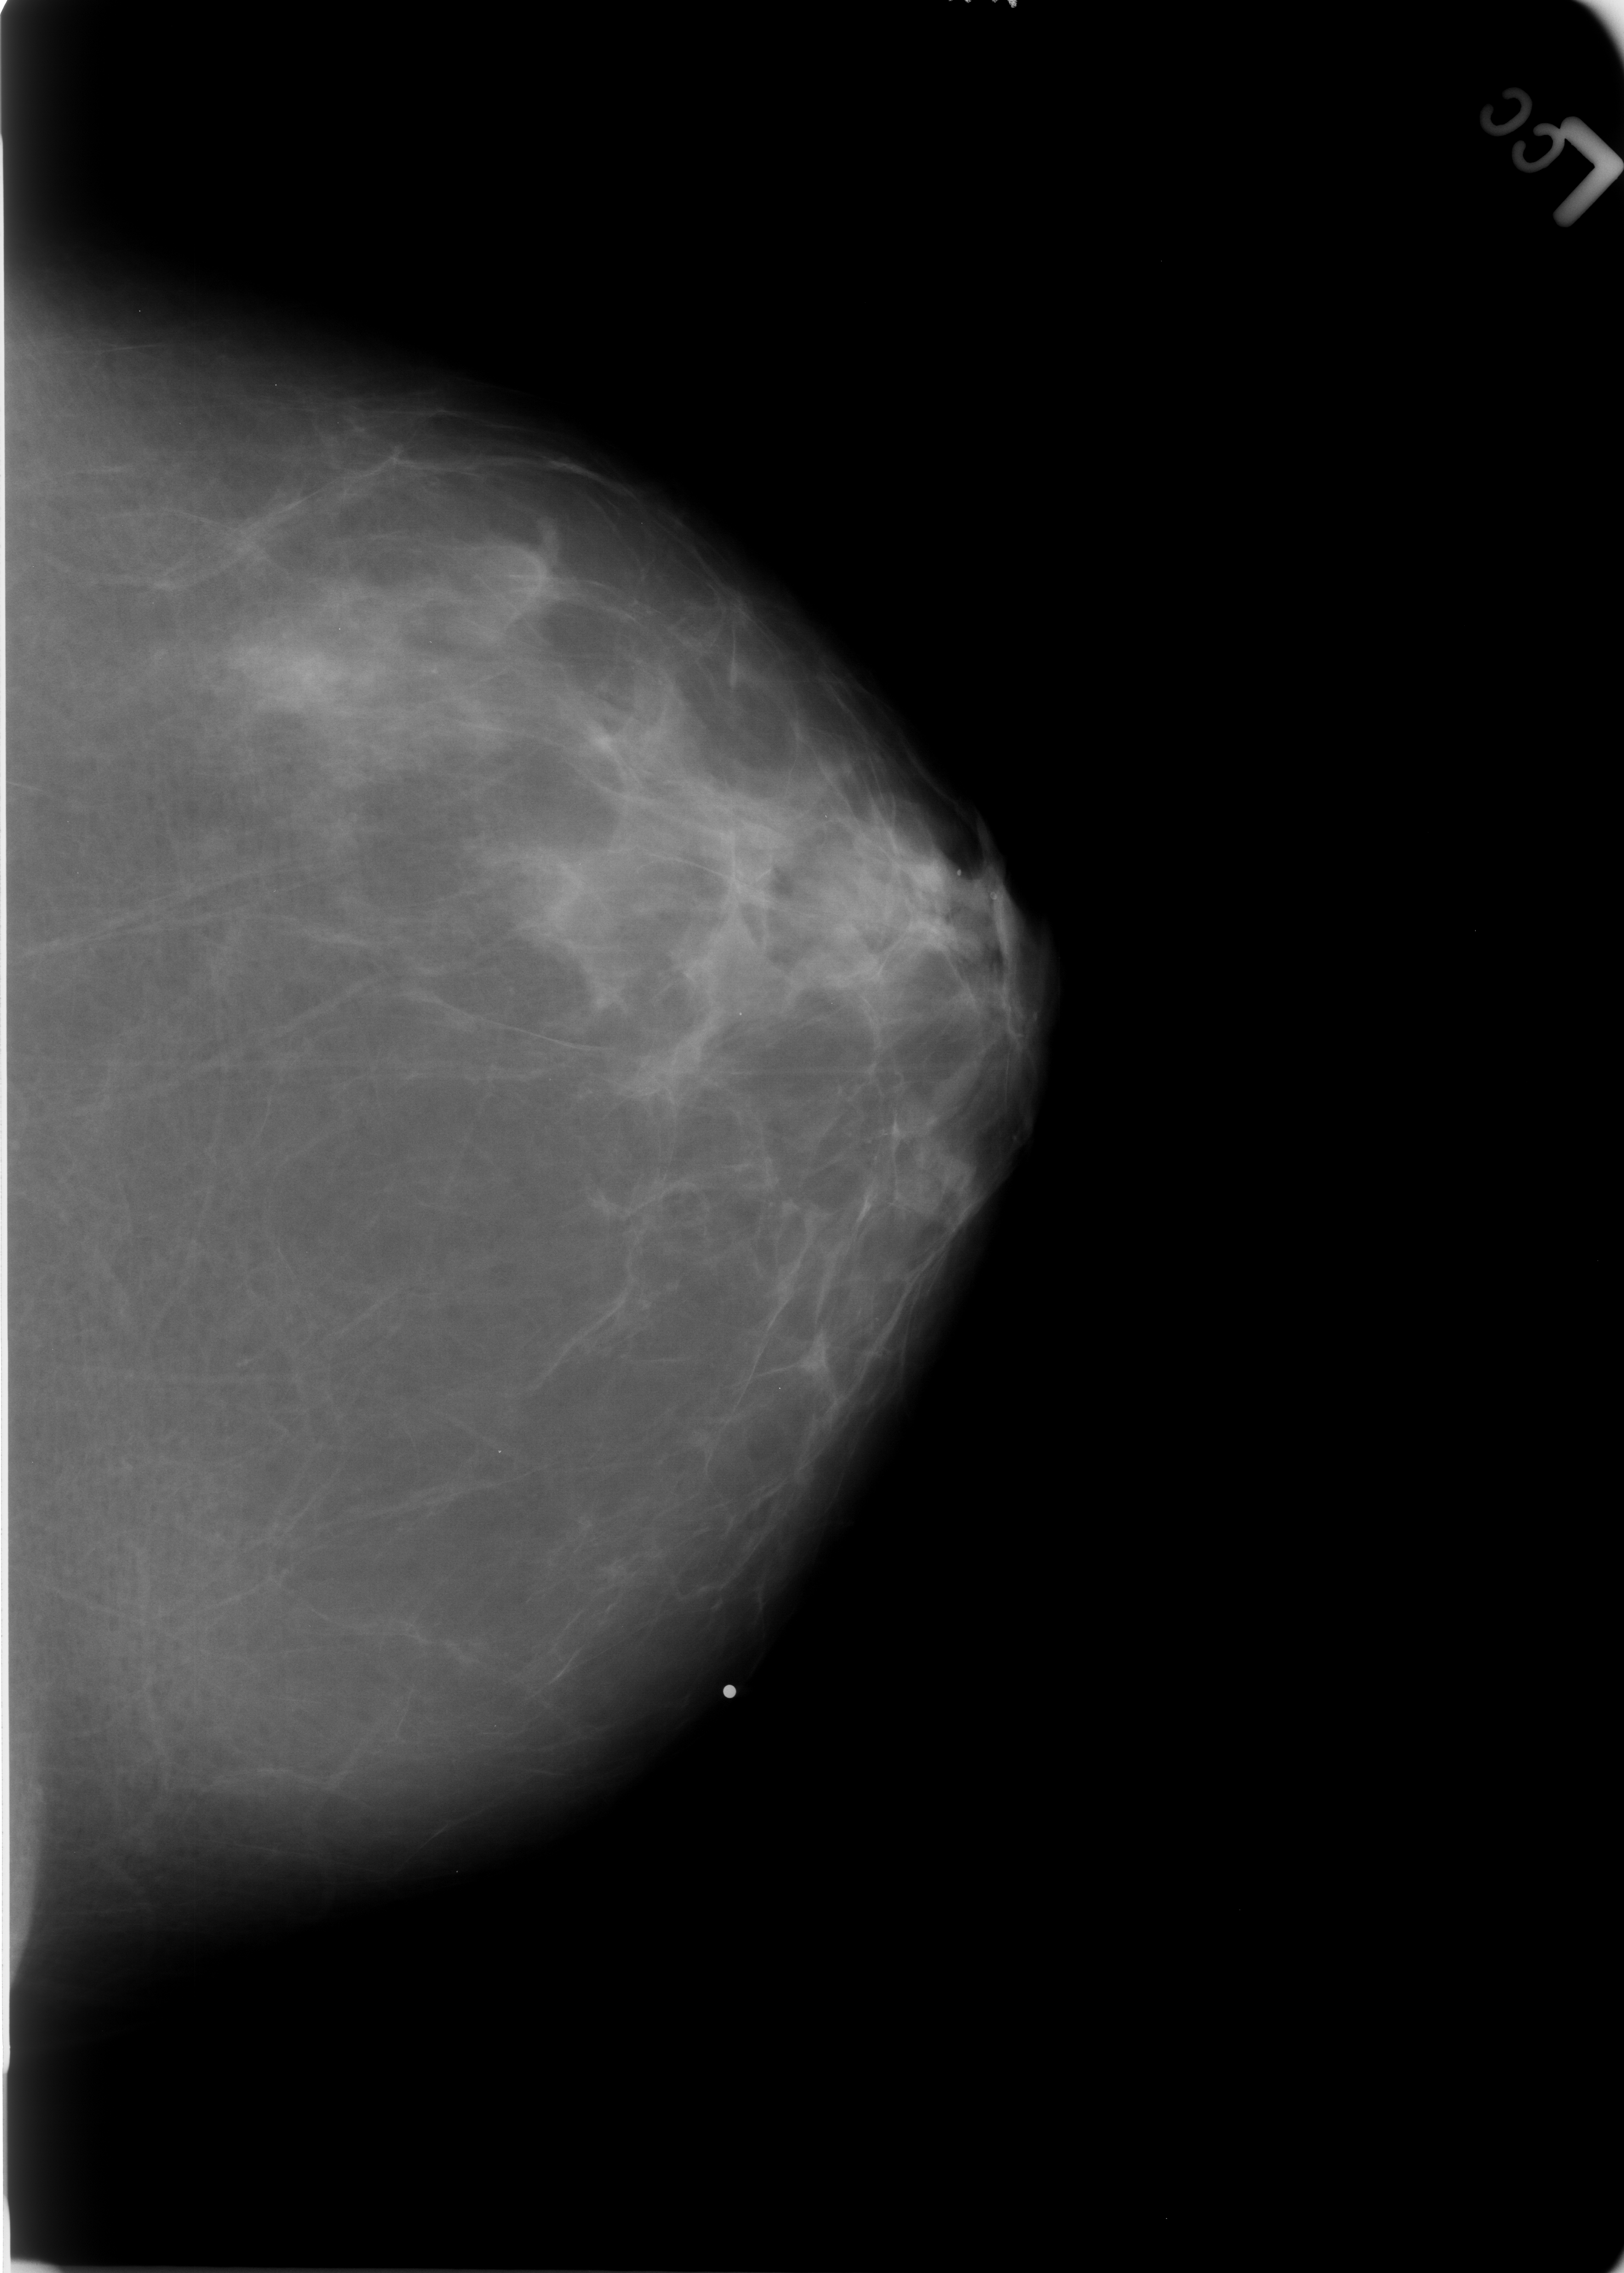
Scanned film-screen mammogram, left breast, CC view, breast composition: scattered fibroglandular densities (BI-RADS density category 2 of 4).
Radiologist-marked abnormalities on this image: Finding 1 of 2: calcifications, morphology lucent center / punctate; BI-RADS assessment category 2; subtlety rating 5 on a 1 (subtle) to 5 (obvious) scale; benign without callback (not worked up further). Finding 2 of 2: calcifications, morphology lucent center / punctate; BI-RADS assessment category 2; benign without callback (not worked up further).